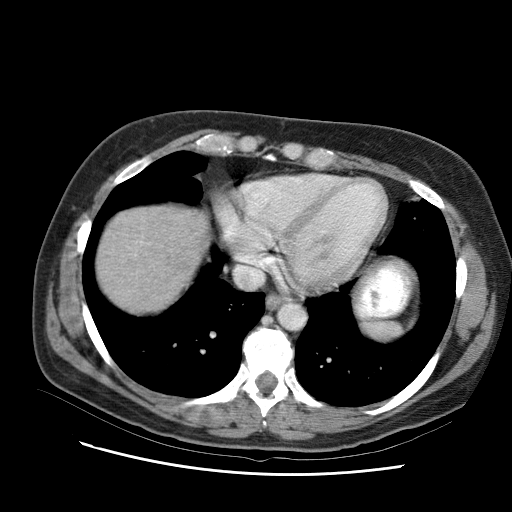
Contrast-enhanced abdominal CT (liver protocol), one axial slice. Slice 87 of 95 in the series (ordered by position). One of 2 acquisitions stored at this slice position. Soft-tissue window (W 400 / L 40 HU). 512 × 512 image matrix, field of view 360 × 360 mm. Case-level facts recorded for this patient, not image findings: diagnosis: hepatocellular carcinoma (patient treated with transarterial chemoembolisation; whether this scan precedes or follows treatment is not stated here); TNM stage (as recorded): Stage-I.
Annotated regions visible in this slice (semi-automatic segmentation, software-assisted and operator-edited):
- liver parenchyma outside the tumour (the mass and vessels are separate outlines, so this box may not span the whole liver): bounding box [x1, y1, x2, y2] px = [110, 212, 180, 280]